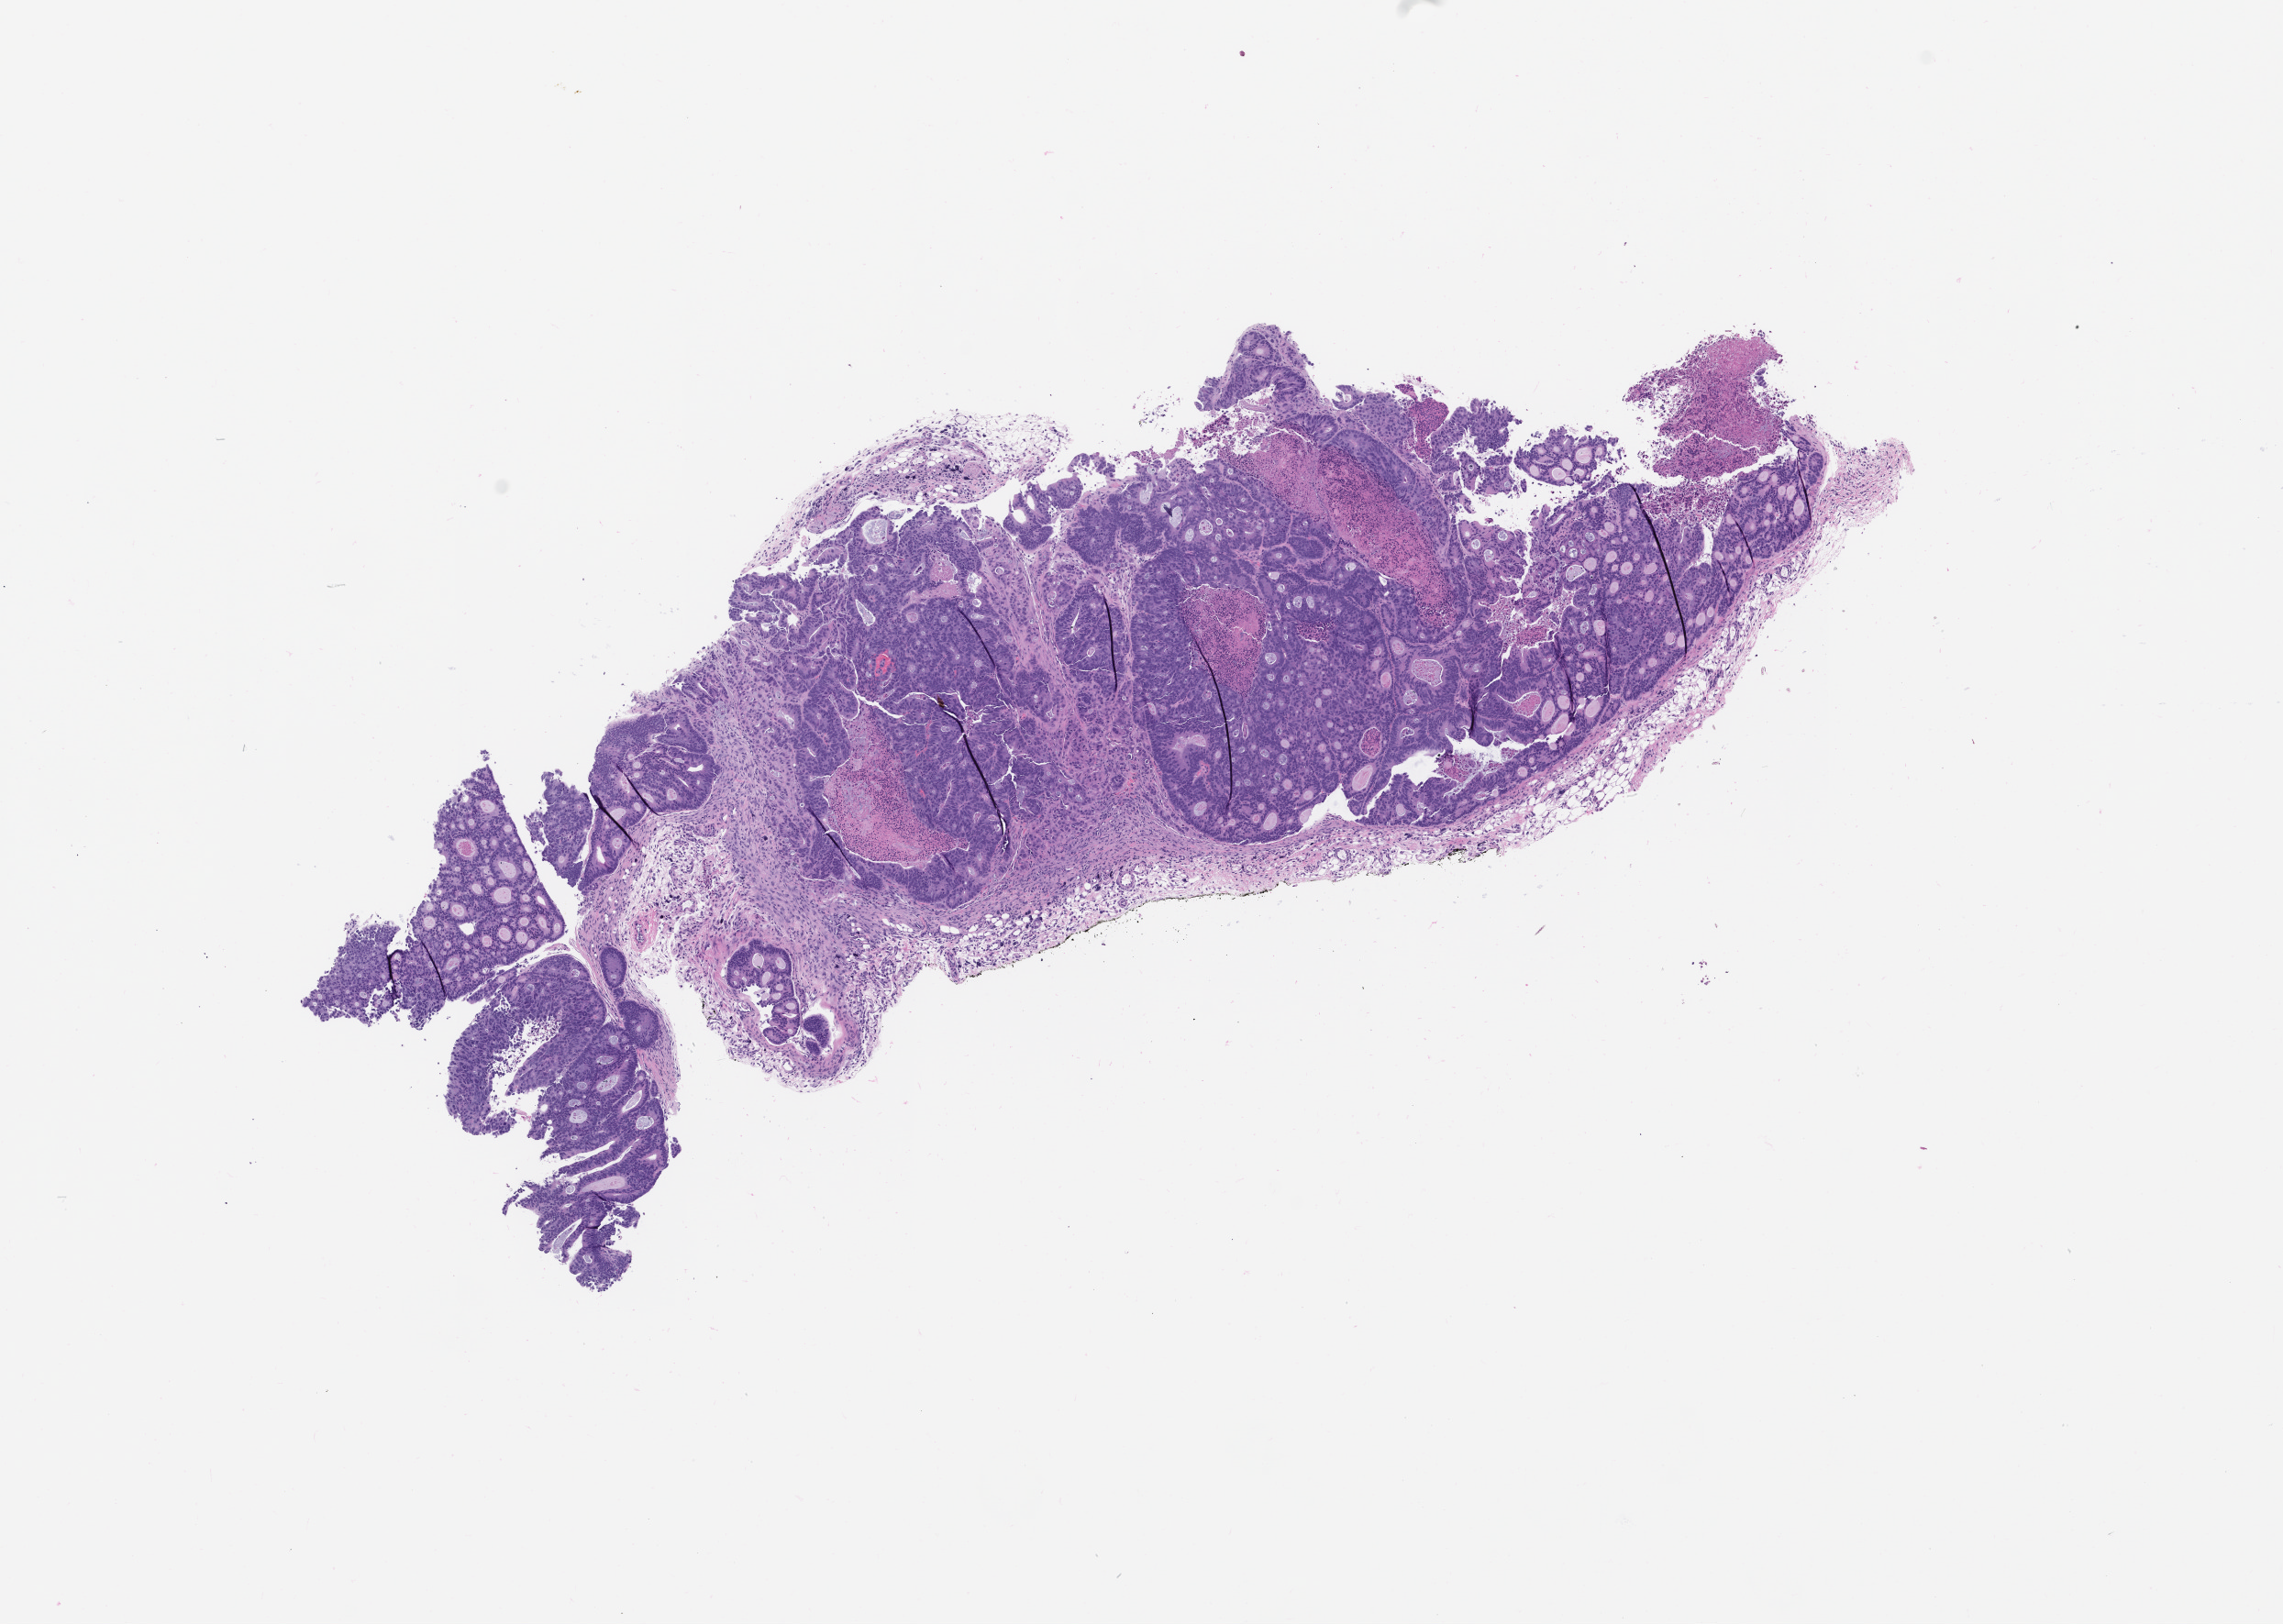
H&E whole-slide image of a patient-derived xenograft (PDX) tumor grown in a mouse, passage 0, a low-resolution overview of the entire scanned area, about 10.0 x 7.1 mm. FFPE section. Originating tumor site category: colon.
* originating patient diagnosis: Colon Adenocarcinoma